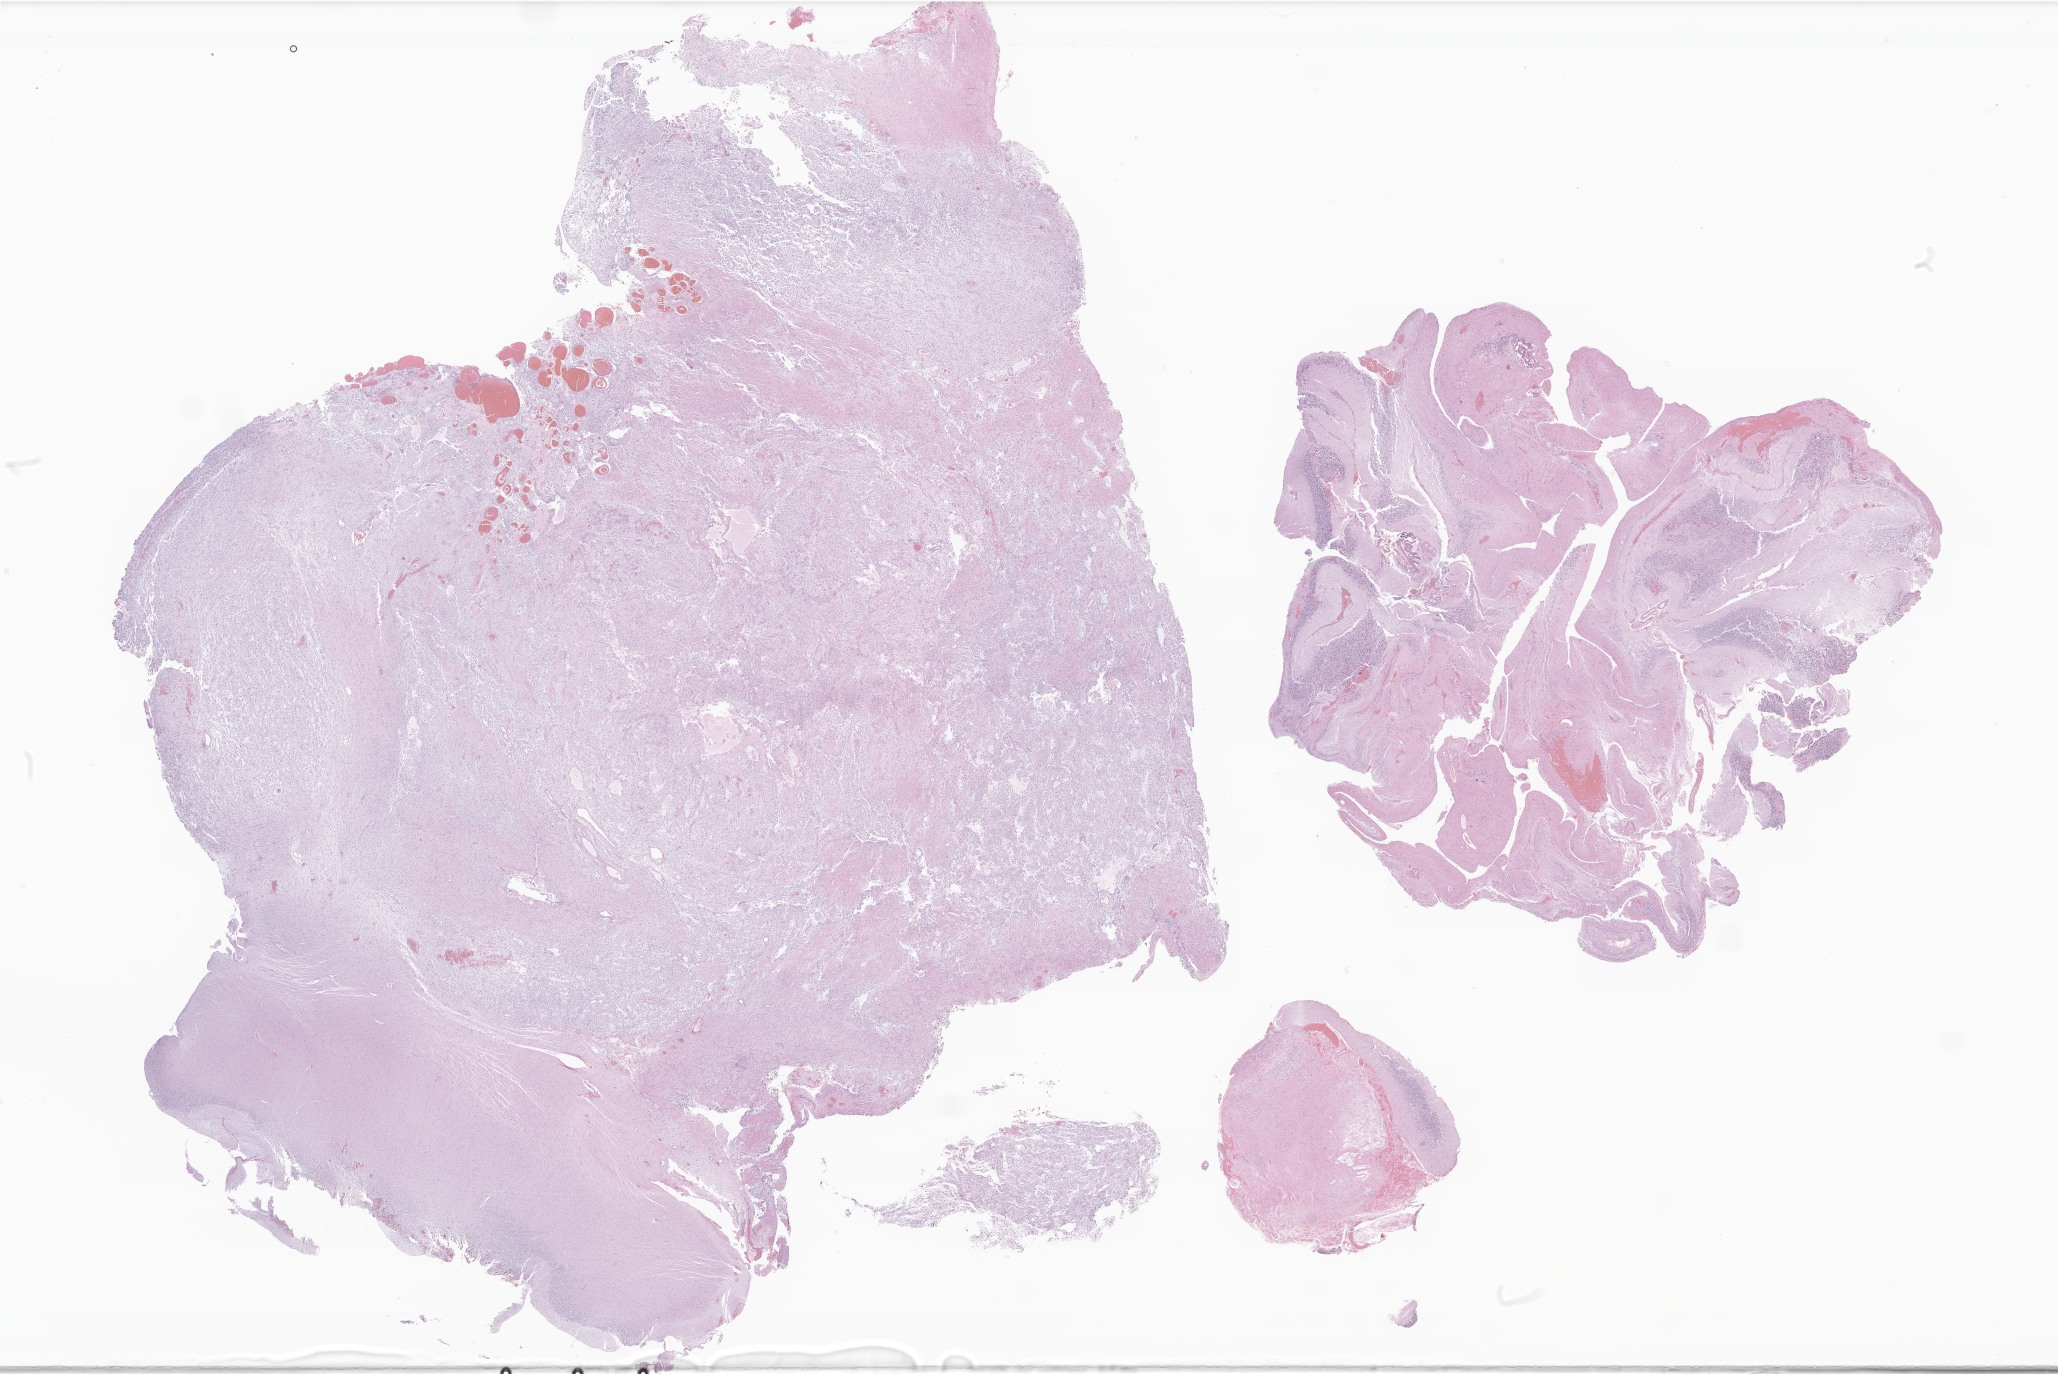
Digitized H&E-stained section of tumor tissue from the brain, a low-resolution overview of the entire scanned area, about 34.7 x 23.2 mm; formalin-fixed, paraffin-embedded (FFPE) tissue. Patient: female, age 121 months (10 years 1 month).
Diagnosis: Neoplasm, malignant.